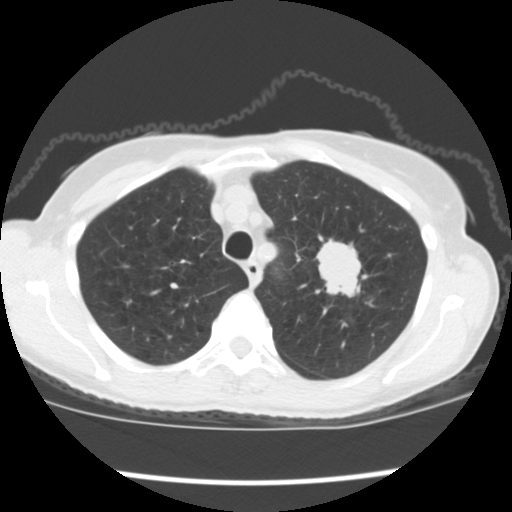
Low-dose screening chest CT, one axial slice. Position 143 of 176 along the scan axis. 120 kVp. Lung window (W 1500 / L -600 HU). 2.5 mm slice thickness. 512 × 512 image matrix, field of view 318 × 318 mm.
Annotated regions visible in this slice (expert manual segmentation):
- lesion 1 (tumor, upper lobe of left lung): box from (x=316, y=239) to (x=361, y=297) px